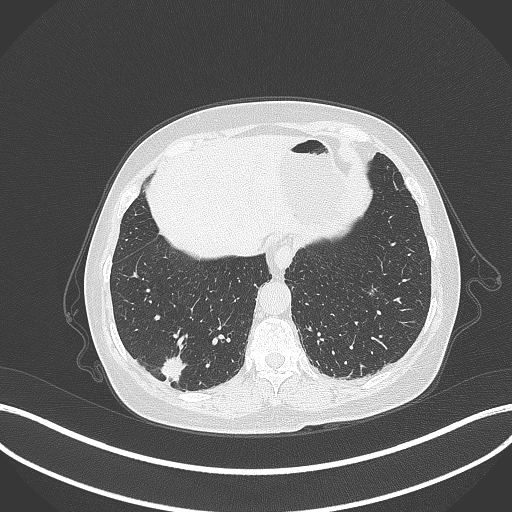
Chest CT, one axial slice. Position 60 of 333 along the scan axis. Reconstruction kernel B70f. Lung window (W 1500 / L -600 HU). 1 mm slice thickness. 512 × 512 image matrix, field of view 400 × 400 mm. Female patient, age 69 years. Case-level facts recorded for this patient, not image findings: clinical TNM (as recorded): T1b N0 M0.
Outlined on this slice (rectangle marked by the reading radiologist):
- lung tumour (recorded histology: adenocarcinoma): bounding box <160,352,183,383> (left, top, right, bottom; pixels)